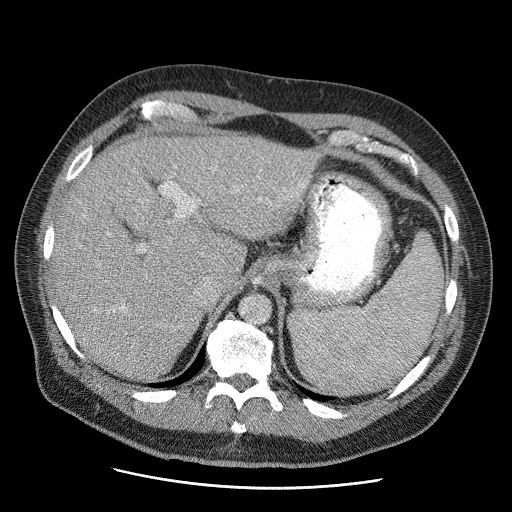
Contrast-enhanced abdominal CT (liver protocol), one axial slice. Slice 39 of 81 in the series (ordered by position). Reconstruction kernel STANDARD. Soft-tissue window (W 400 / L 40 HU). 2.5 mm slice thickness. 512 × 512 image matrix, field of view 380 × 380 mm. From the clinical record (not read from this slice): diagnosis: hepatocellular carcinoma (patient treated with transarterial chemoembolisation; whether this scan precedes or follows treatment is not stated here); TNM stage (as recorded): Stage-IIIA; Child-Pugh class: A; tumour differentiation: moderately differentiated; tumour size: 5.5 cm.
Annotated regions visible in this slice (semi-automatically segmented with operator editing):
- liver parenchyma outside the tumour (the mass and vessels are separate outlines, so this box may not span the whole liver): bounding box (x1, y1, x2, y2) in pixels: (52, 132, 318, 380)
- liver vessels: (108, 182, 304, 309)